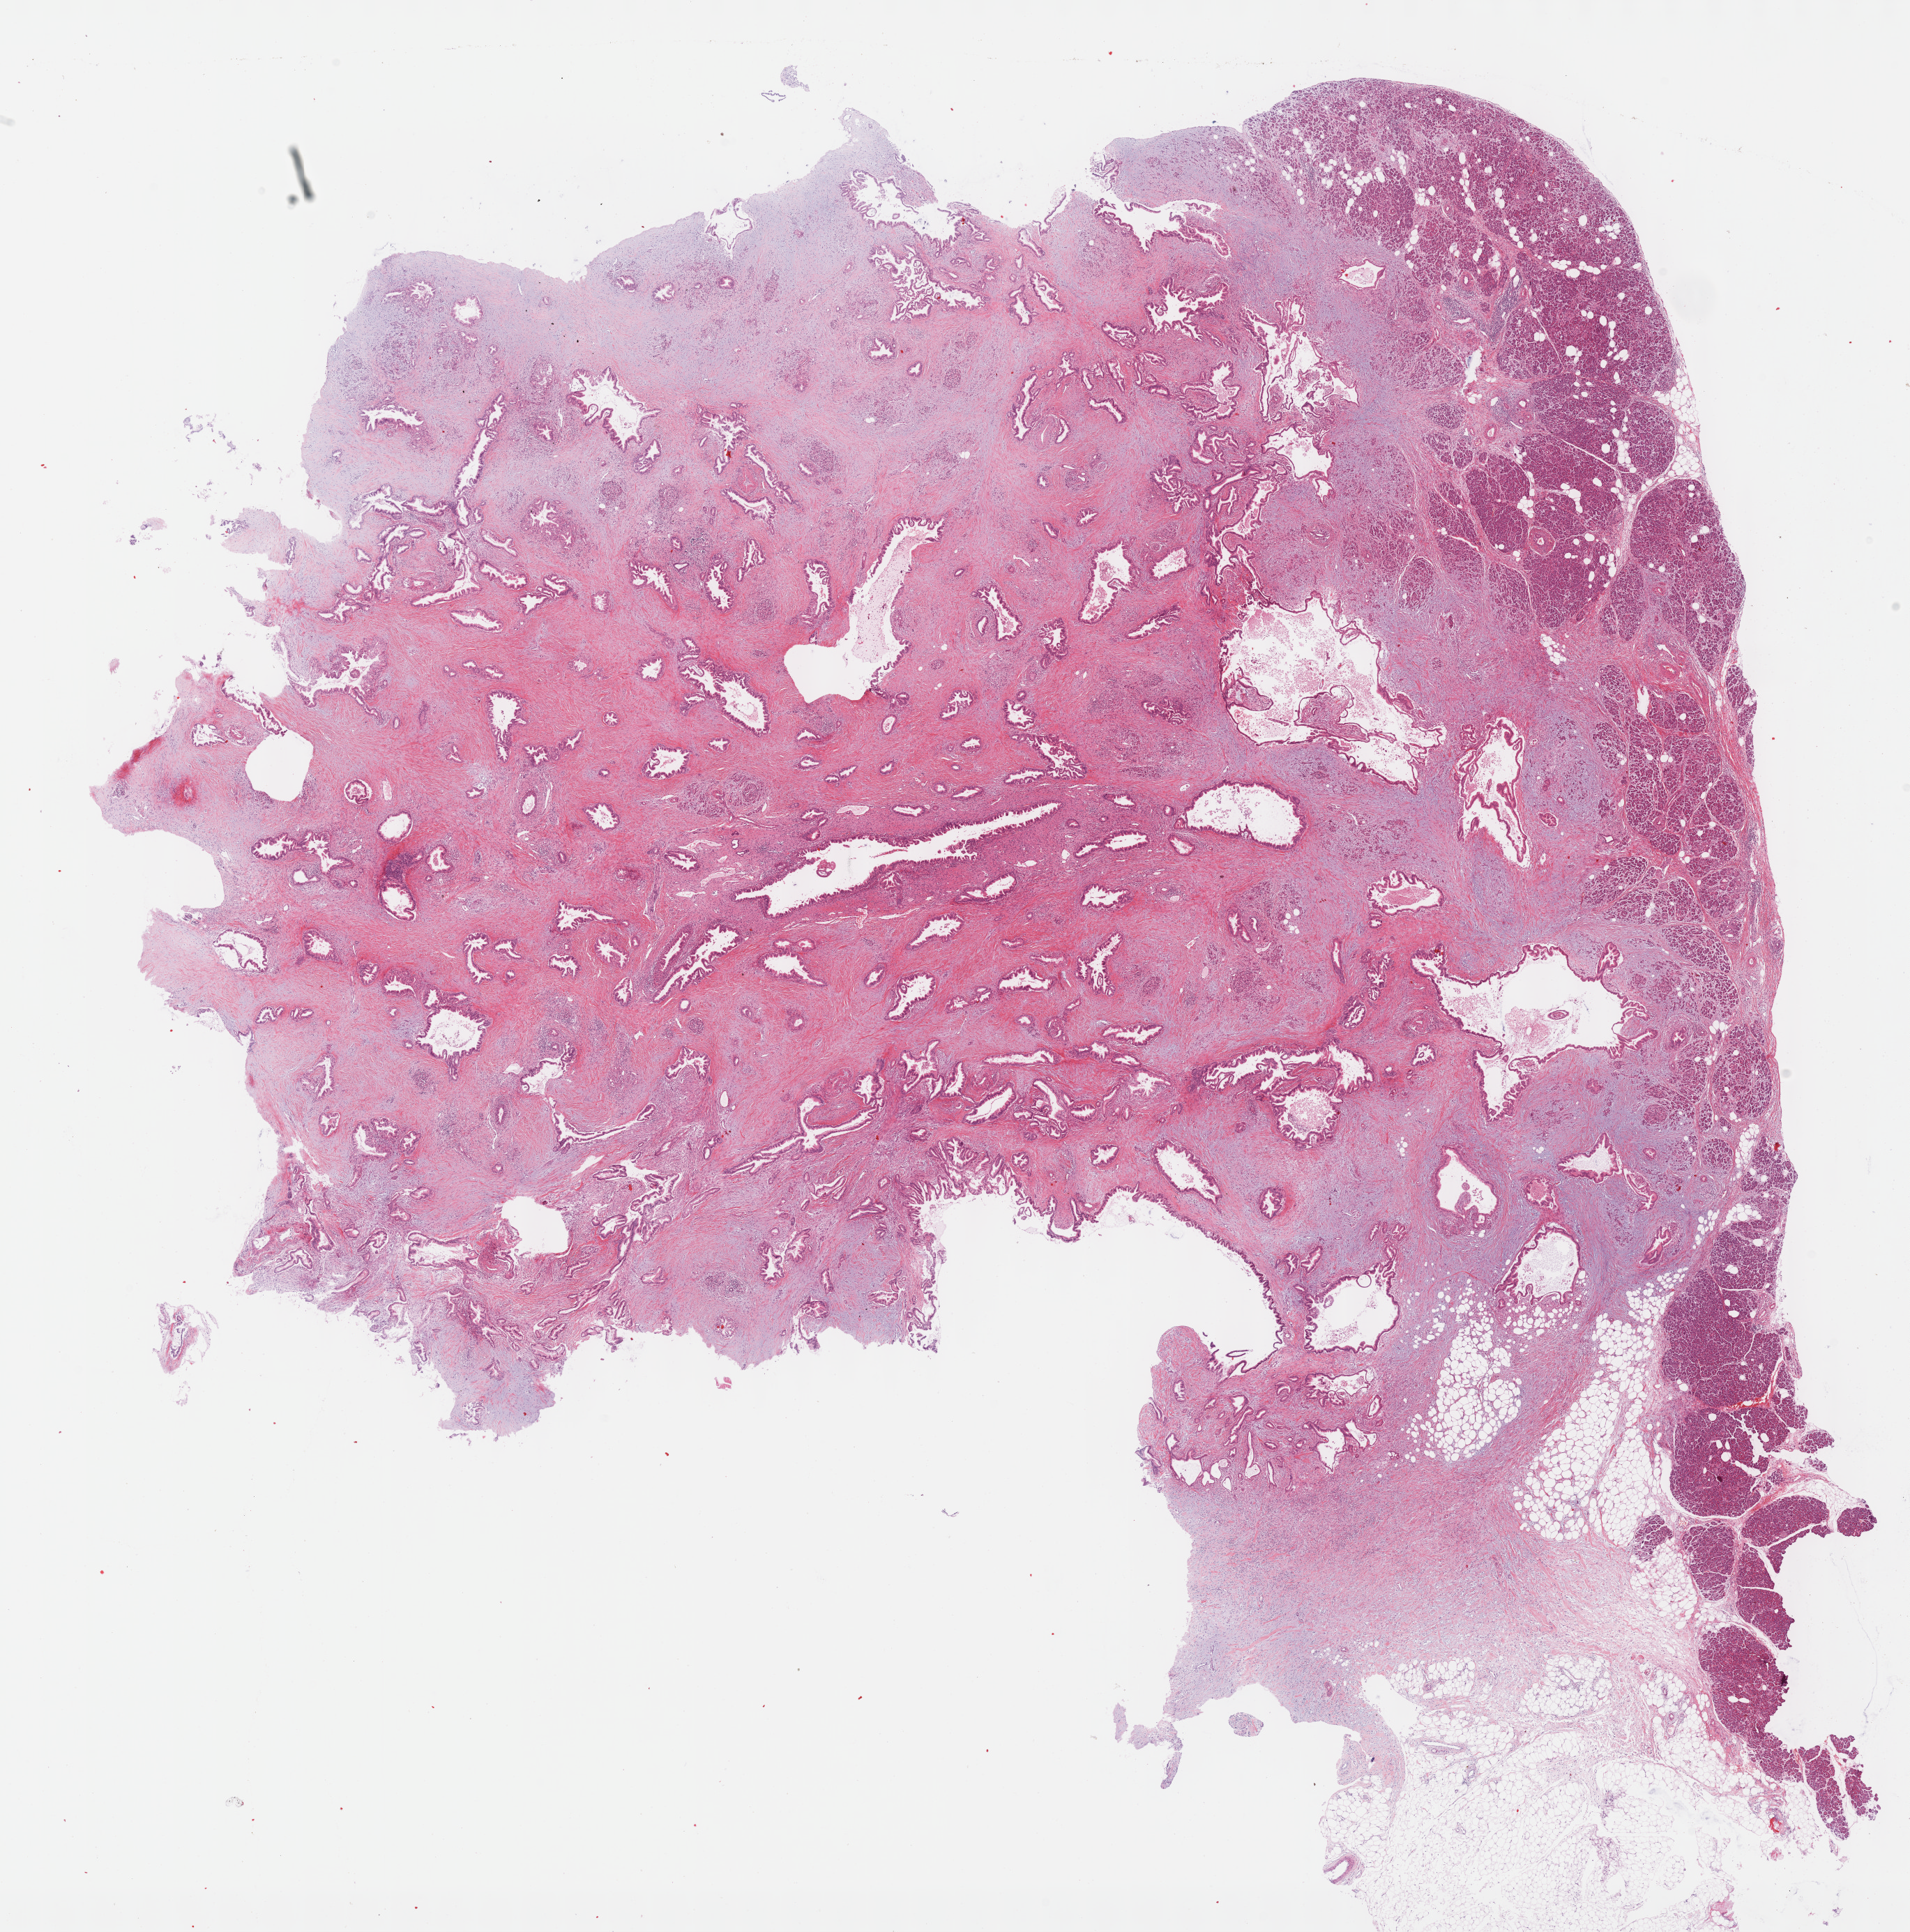
Digitized Hematoxylin and eosin (H&E) stained tissue section (whole slide), low-resolution overview of the scanned area, about 22.1 x 22.4 mm (slide scanned at 40x); formalin-fixed paraffin-embedded (FFPE) diagnostic section; primary tumour sample from the pancreas. Female patient; age at initial diagnosis 72 years. Histologic grade: G2 (moderately differentiated).
Lymph nodes positive (case pathology): 1 of 18 examined. TNM: T3 N0 MX. AJCC pathologic stage: IIA (7th edition). Pathologic diagnosis: Infiltrating duct carcinoma, NOS (tail of pancreas).